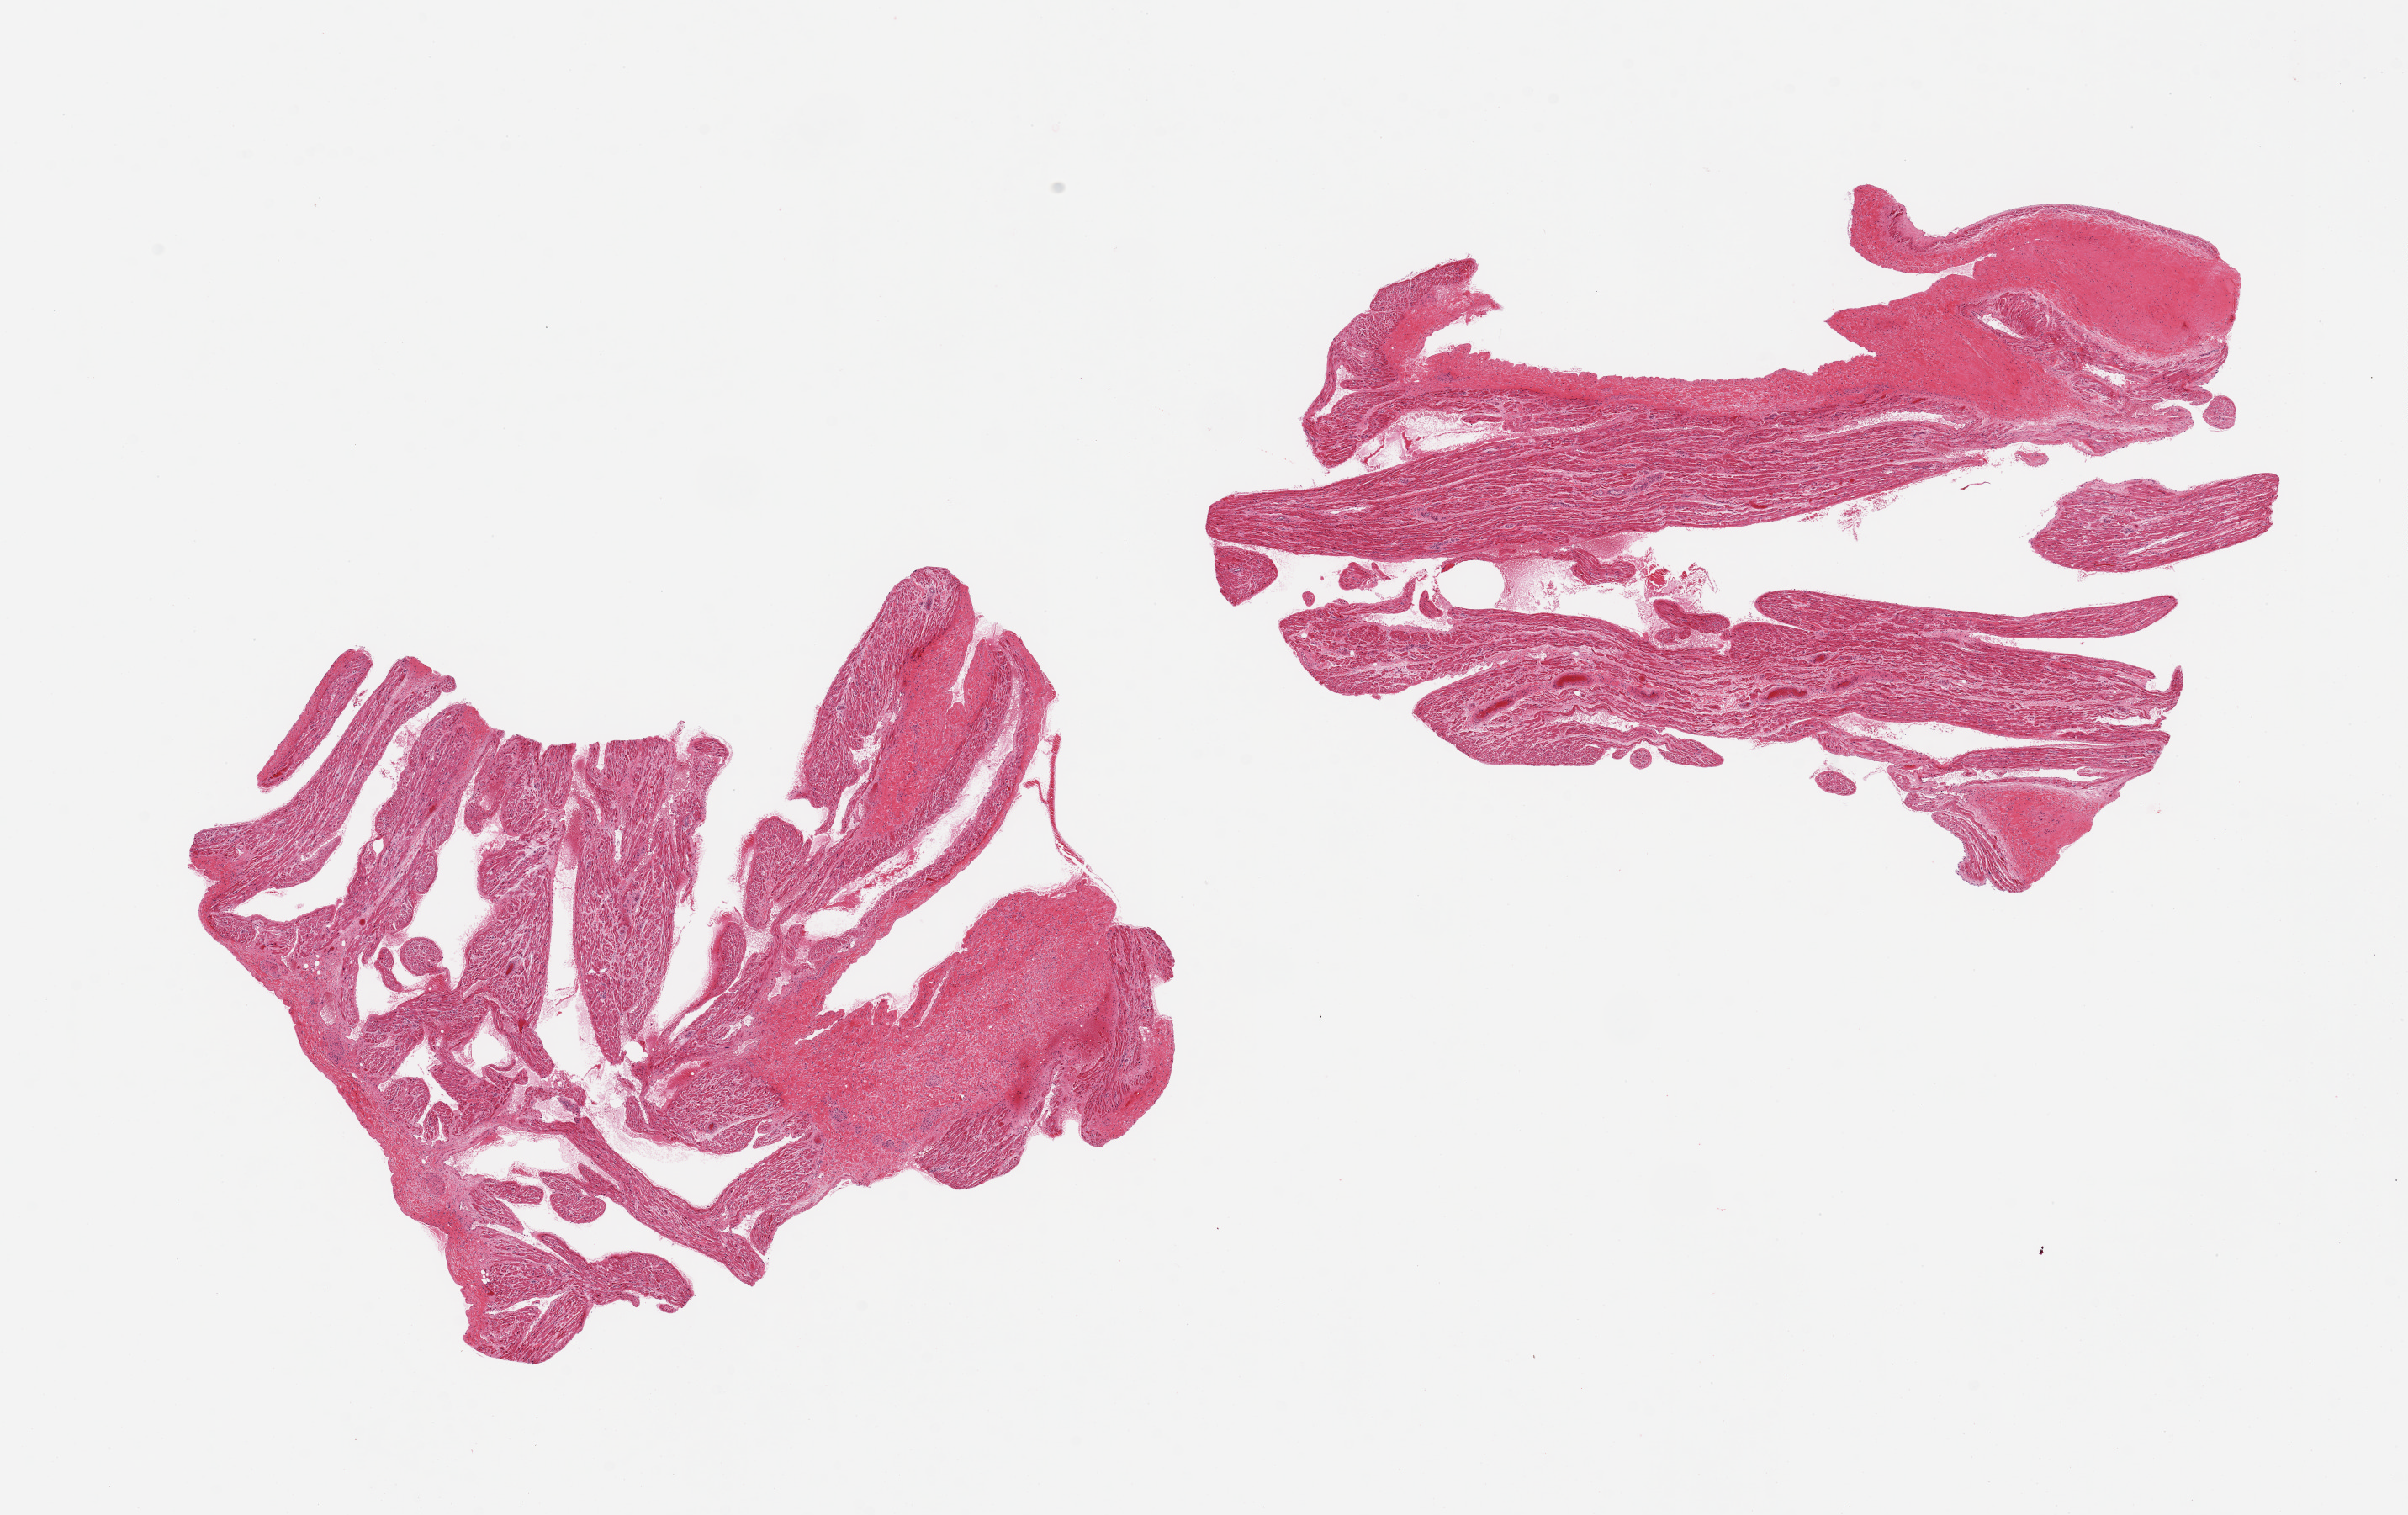
H&E whole-slide image, a low-resolution overview of the entire scanned area, about 22.6 x 14.2 mm (from a 20x scan). PAXgene-fixed paraffin-embedded (PFPE) section. Target tissue: auricular appendage. Tissue donor sample. Donor sex: male.
Reviewer comment on this tissue sample: 2 pieces; Focally thick pericardial fibrous tissue in both.